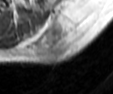
MRI of an extremity soft-tissue mass, one axial slice. Slice 32 of 42 in the series (ordered by position). MR volume resampled by the dataset authors to the PET/CT grid (not the native acquisition matrix). 3.27 mm slice thickness. 113 × 94 image matrix, field of view 110 × 92 mm. Male patient. Case-level facts recorded for this patient, not image findings: histological type: leiomyosarcoma; grade: intermediate; site of the primary tumour: left pelvis.
Outlined on this slice (expert contour drawn on MRI and transferred to this co-registered scan by the dataset authors):
- gross tumour volume (mass): bounding box (x1, y1, x2, y2) in pixels: (33, 18, 82, 63)